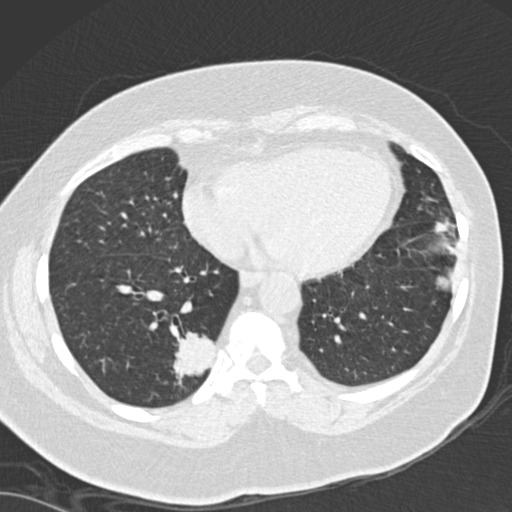
Axial slice from a low-dose chest CT screening exam, baseline screening round, lung window (W 1500 / L -600 HU), 2 mm slice thickness, standard (soft-tissue) reconstruction kernel (B30f), 120 kVp. Female, age 66 years at enrolment.
Expert-annotated lung lesion, bounding box (x1, y1, x2, y2) in pixels: (145, 314, 235, 407). The screening reader recorded 3 non-calcified nodules or masses ≥4 mm on this exam (left lower lobe, left lower lobe, right lower lobe); which of them this box marks is not recorded. Official screen result: positive, change unspecified: nodule(s) >= 4 mm or enlarging nodule(s), mass(es), or other non-specific abnormalities suspicious for lung cancer. Participant outcome: lung cancer diagnosed 67 days after this screen — adenocarcinoma, NOS, right lower lobe, well differentiated (G1), stage IB (AJCC 6th edition), 55 mm at pathology.